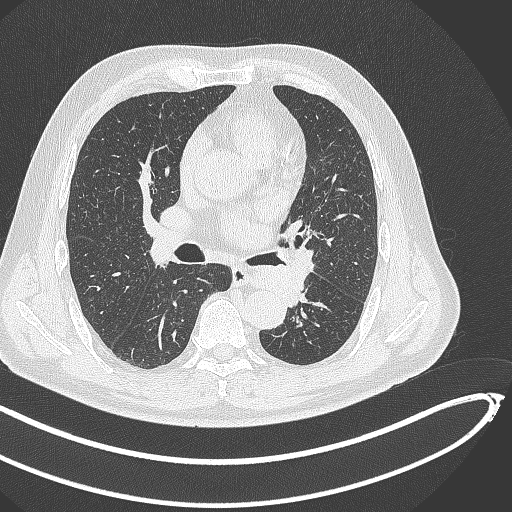
Chest CT, one axial slice. Lung window (W 1500 / L -600 HU). 1 mm slice thickness. 512 × 512 image matrix. Patient: male, 64 years. From the clinical record (not read from this slice): clinical TNM (as recorded): T1c N0 M0; histopathological grade: G2.
Outlined on this slice (rectangle marked by the reading radiologist):
- lung tumour (recorded histology: squamous cell carcinoma): bounding box <248,251,319,311> (left, top, right, bottom; pixels)